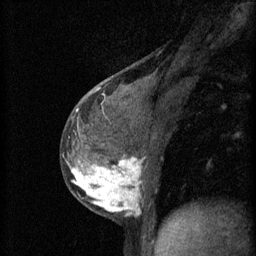
Breast MRI (dynamic contrast-enhanced), one sagittal slice; slice 29 of 60 in the series (ordered by position); 3 images stored at this slice position (order not interpretable as contrast timing); 1.5 T; TE 4.2 ms, TR 11 ms; 2 mm slice thickness; 256 × 256 image matrix, field of view 180 × 180 mm. Female patient, age 37 years.
Annotated regions visible in this slice (semi-automatic segmentation, software-assisted and operator-edited):
- analysis volume of interest (the breast-tissue region the enhancement analysis was run in; not a lesion): bounding box [x1, y1, x2, y2] px = [66, 138, 173, 221]
- tumour enhancement mask (voxels above the 70 % enhancement threshold inside the analysis volume of interest): [70, 158, 143, 215]